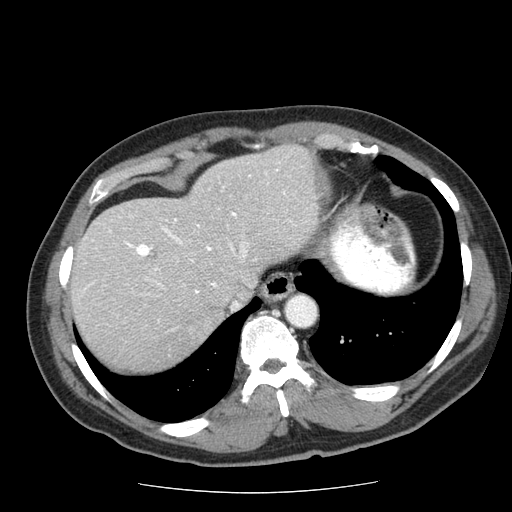
Contrast-enhanced abdominal CT (liver protocol), one axial slice. Slice 53 of 85 in the series (ordered by position). Reconstruction kernel STANDARD. 120 kVp. Soft-tissue window (W 400 / L 40 HU). 512 × 512 image matrix, field of view 360 × 360 mm. Case-level facts recorded for this patient, not image findings: diagnosis: hepatocellular carcinoma (patient treated with transarterial chemoembolisation; whether this scan precedes or follows treatment is not stated here); TNM stage (as recorded): Stage-IIIA; Child-Pugh class: A; tumour differentiation: well differentiated; tumour nodularity: multinodular.
Structures marked on this image (semi-automatic segmentation, software-assisted and operator-edited):
- liver parenchyma outside the tumour (the mass and vessels are separate outlines, so this box may not span the whole liver): bounding box <70,144,320,370> (left, top, right, bottom; pixels)
- liver vessels: <88,170,285,322>